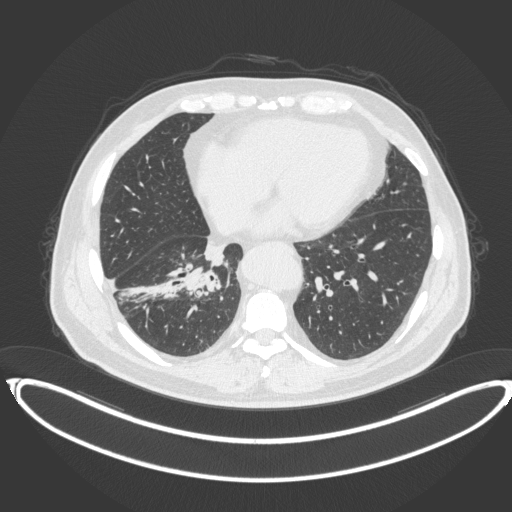
Chest CT, one axial slice; slice 146 of 383 in the series (ordered by position); 120 kVp; lung window (W 1500 / L -600 HU); 1 mm slice thickness; 512 × 512 image matrix, field of view 448 × 448 mm. Patient: male, 61 years. Case-level facts recorded for this patient, not image findings: clinical TNM (as recorded): T1b N1 M0.
Annotated regions visible in this slice (bounding box drawn by a radiologist):
- lung tumour (recorded histology: squamous cell carcinoma): bounding box [x1, y1, x2, y2] px = [184, 265, 222, 297]